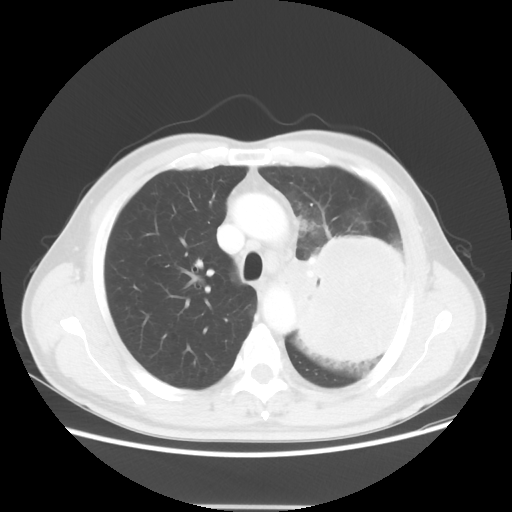
Chest CT, one axial slice; position 38 of 53 along the scan axis; reconstruction kernel STANDARD; lung window (W 1500 / L -600 HU); 5 mm slice thickness; 512 × 512 image matrix, field of view 391 × 391 mm. Male patient, age 60 years. From the clinical record (not read from this slice): clinical TNM (as recorded): T4 N1 M1a.
Structures marked on this image (rectangle marked by the reading radiologist):
- lung tumour (recorded histology: large cell carcinoma): bounding box (x1, y1, x2, y2) in pixels: (282, 228, 422, 364)